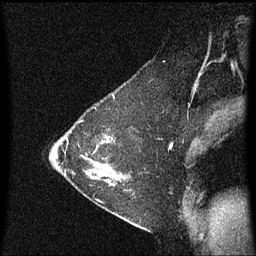
Breast MRI (dynamic contrast-enhanced), one sagittal slice. Dynamic contrast-enhanced series, image 2 of 3 at this slice position (ordered by acquisition). 1.5 T. TE 4.2 ms, TR 8.4 ms. 256 × 256 image matrix, field of view 200 × 200 mm. Patient: female, 36 years. From the clinical record (not read from this slice): setting: breast cancer imaged before/during neoadjuvant chemotherapy; receptor status: HR-positive, HER2-negative.
Annotated regions visible in this slice (semi-automatic segmentation, software-assisted and operator-edited):
- analysis volume of interest (the breast-tissue region the enhancement analysis was run in; not a lesion): box from (x=72, y=118) to (x=123, y=187) px
- tumour enhancement mask (voxels above the 70 % enhancement threshold inside the analysis volume of interest): (x=90, y=138)–(x=121, y=179)